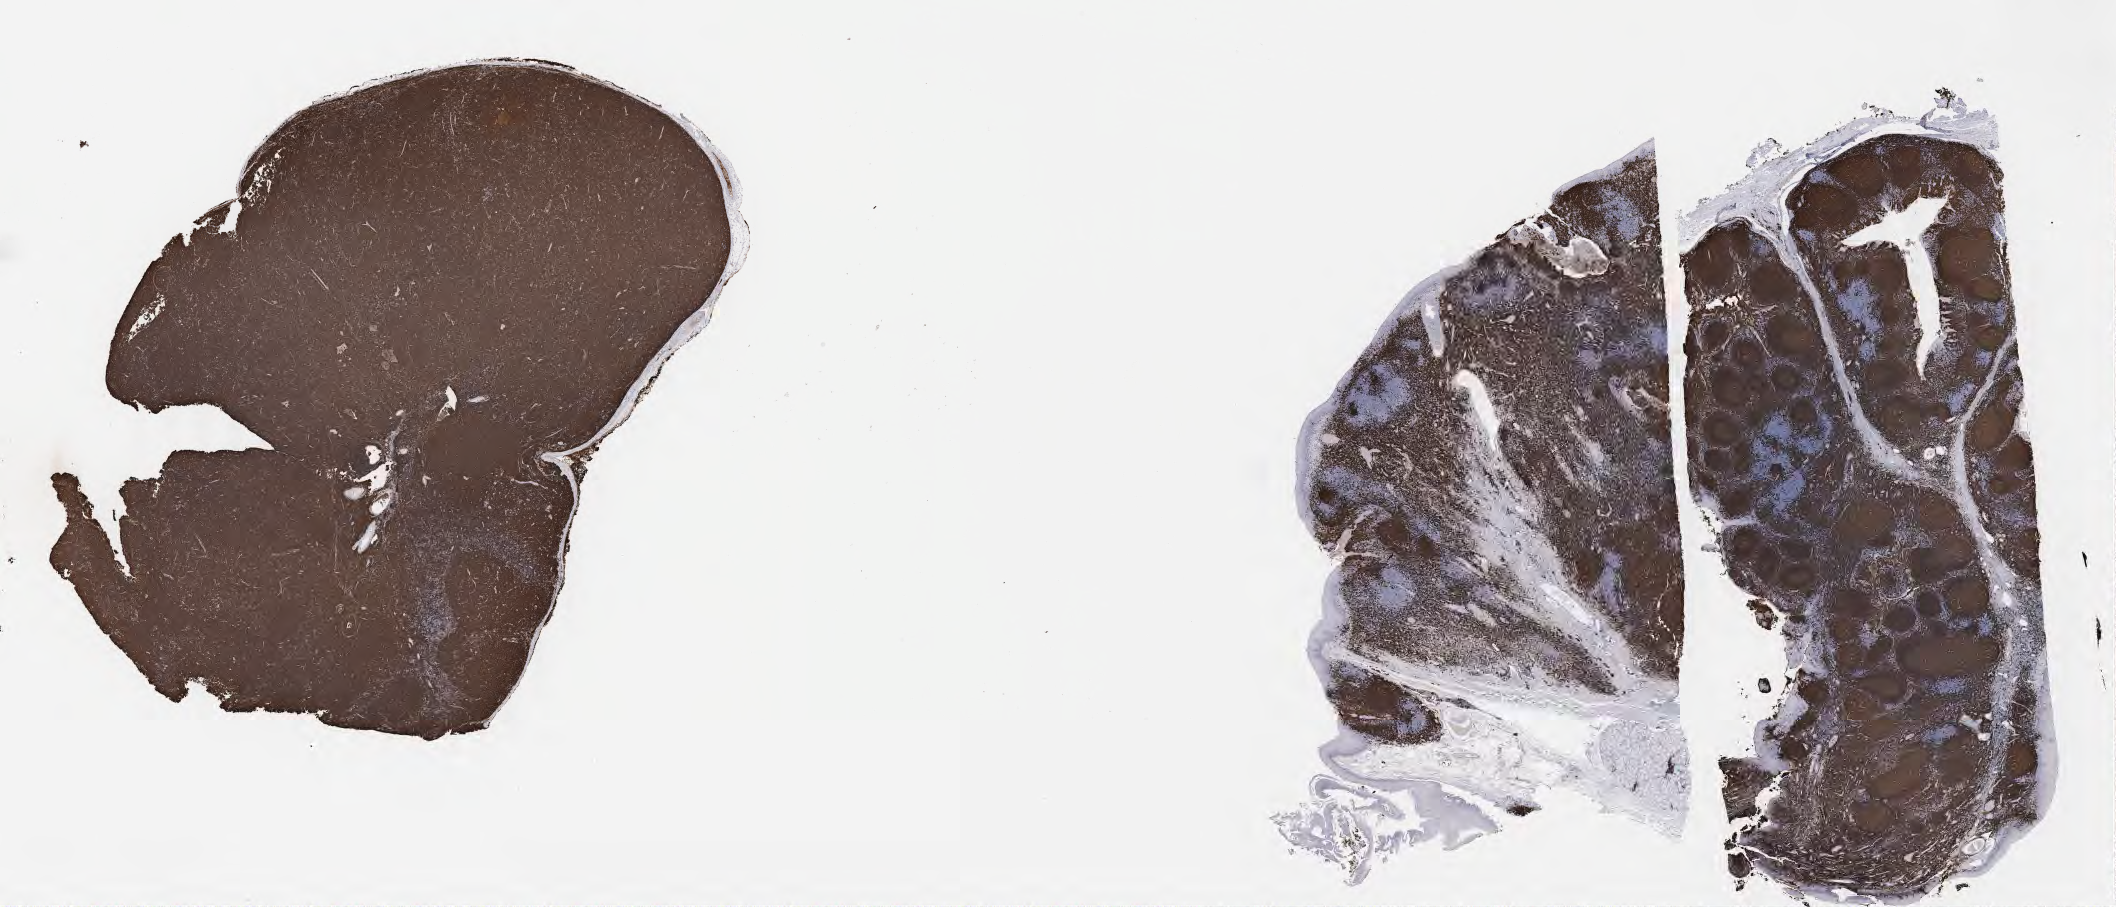
Immunohistochemistry (IHC) whole-slide image stained for CD20, low-resolution overview of the scanned area, about 34.2 x 14.7 mm; tumor tissue; site: lymph node. Patient: male, 32 years old.
Histologic diagnosis: Diffuse large B-cell lymphoma, NOS.